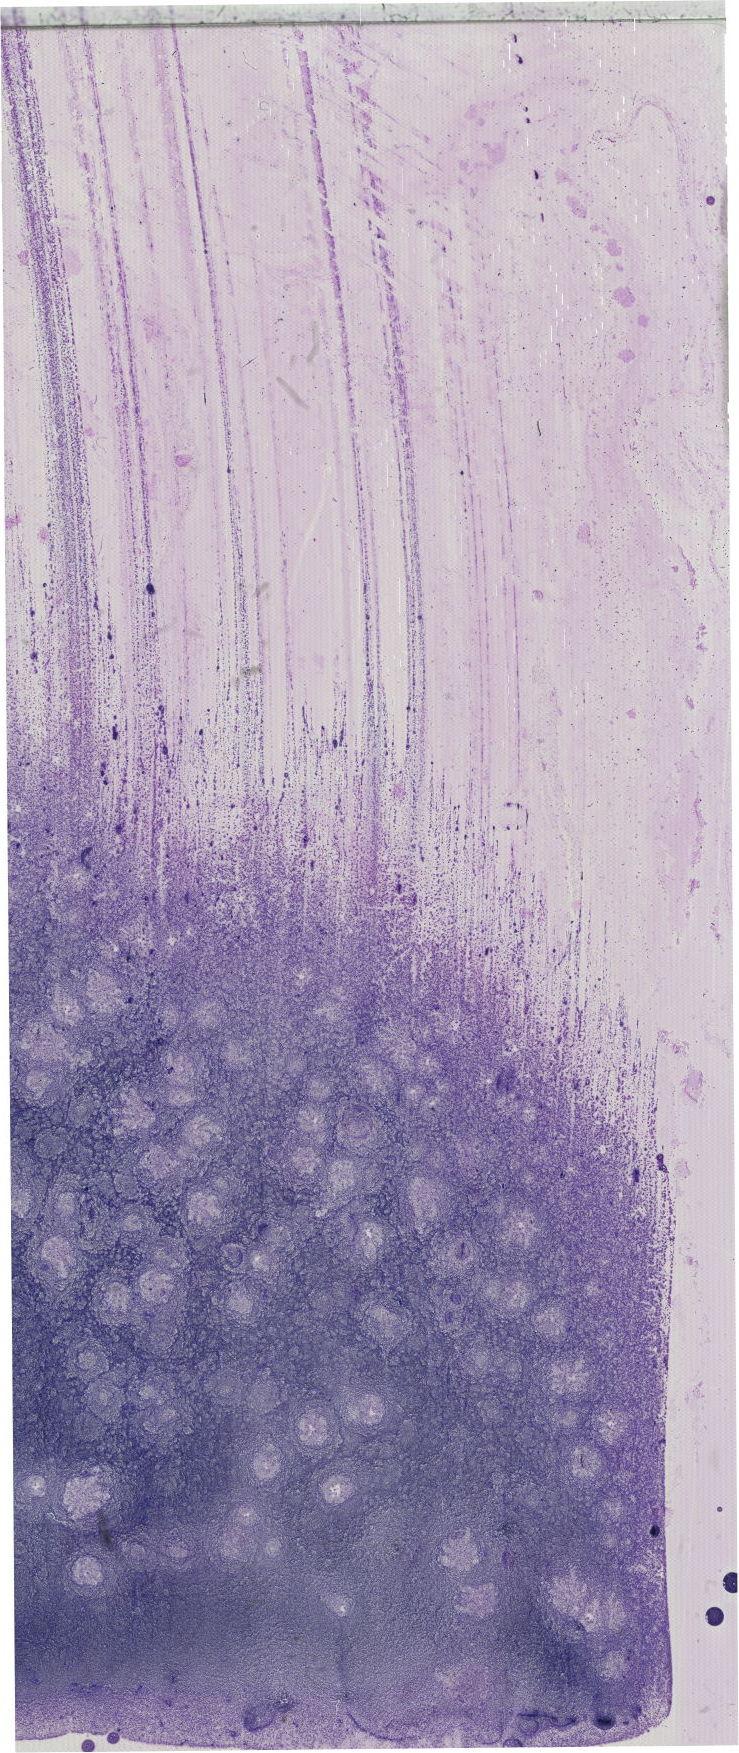
Whole-slide image of a May-Grünwald–Giemsa-stained bone marrow aspirate smear — a low-resolution overview of the entire scanned area, about 20.9 x 49.7 mm. Female patient.
Diagnosis: Chronic Phase Chronic Myeloid Leukemia, BCR-ABL1 Positive.